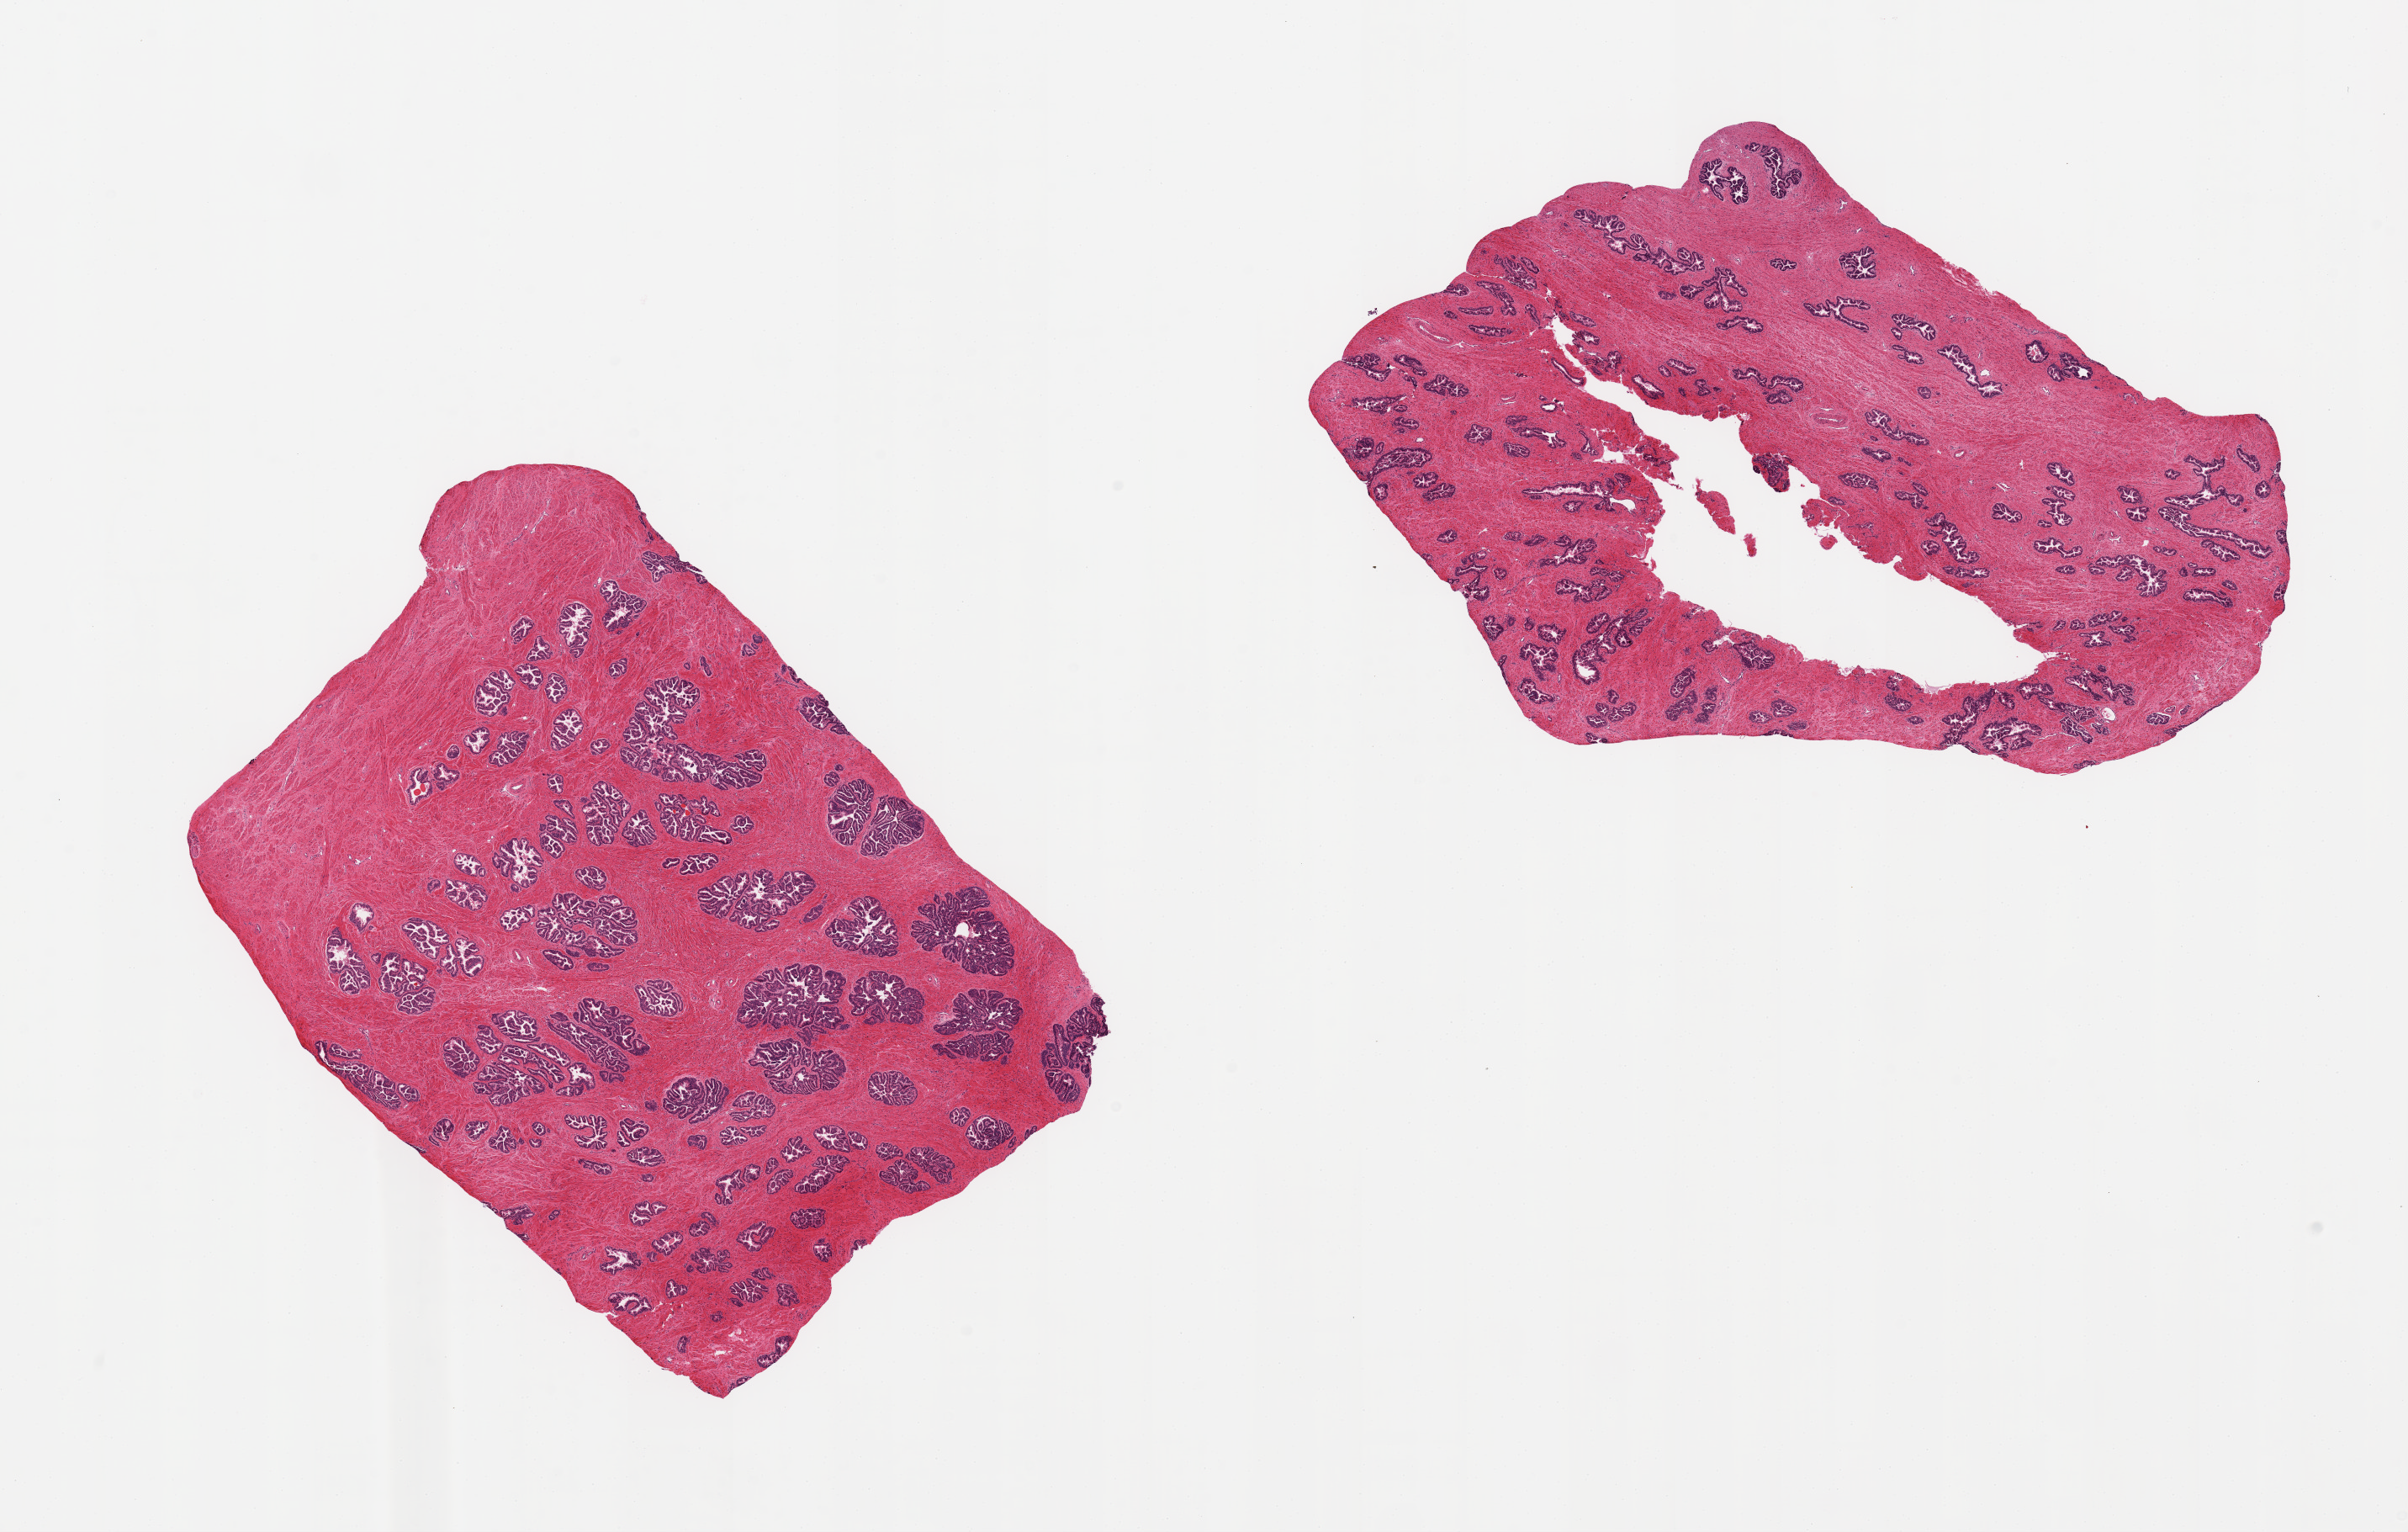
Digitized H&E-stained section — whole scanned area (about 22.6 x 14.4 mm) shown as a low-resolution overview, PAXgene-fixed paraffin-embedded (PFPE) section, sampled site (target tissue): prostate, donor tissue sample. Donor: male.
• reviewer comment on this tissue sample: 2 pieces, glandular hyerplasia